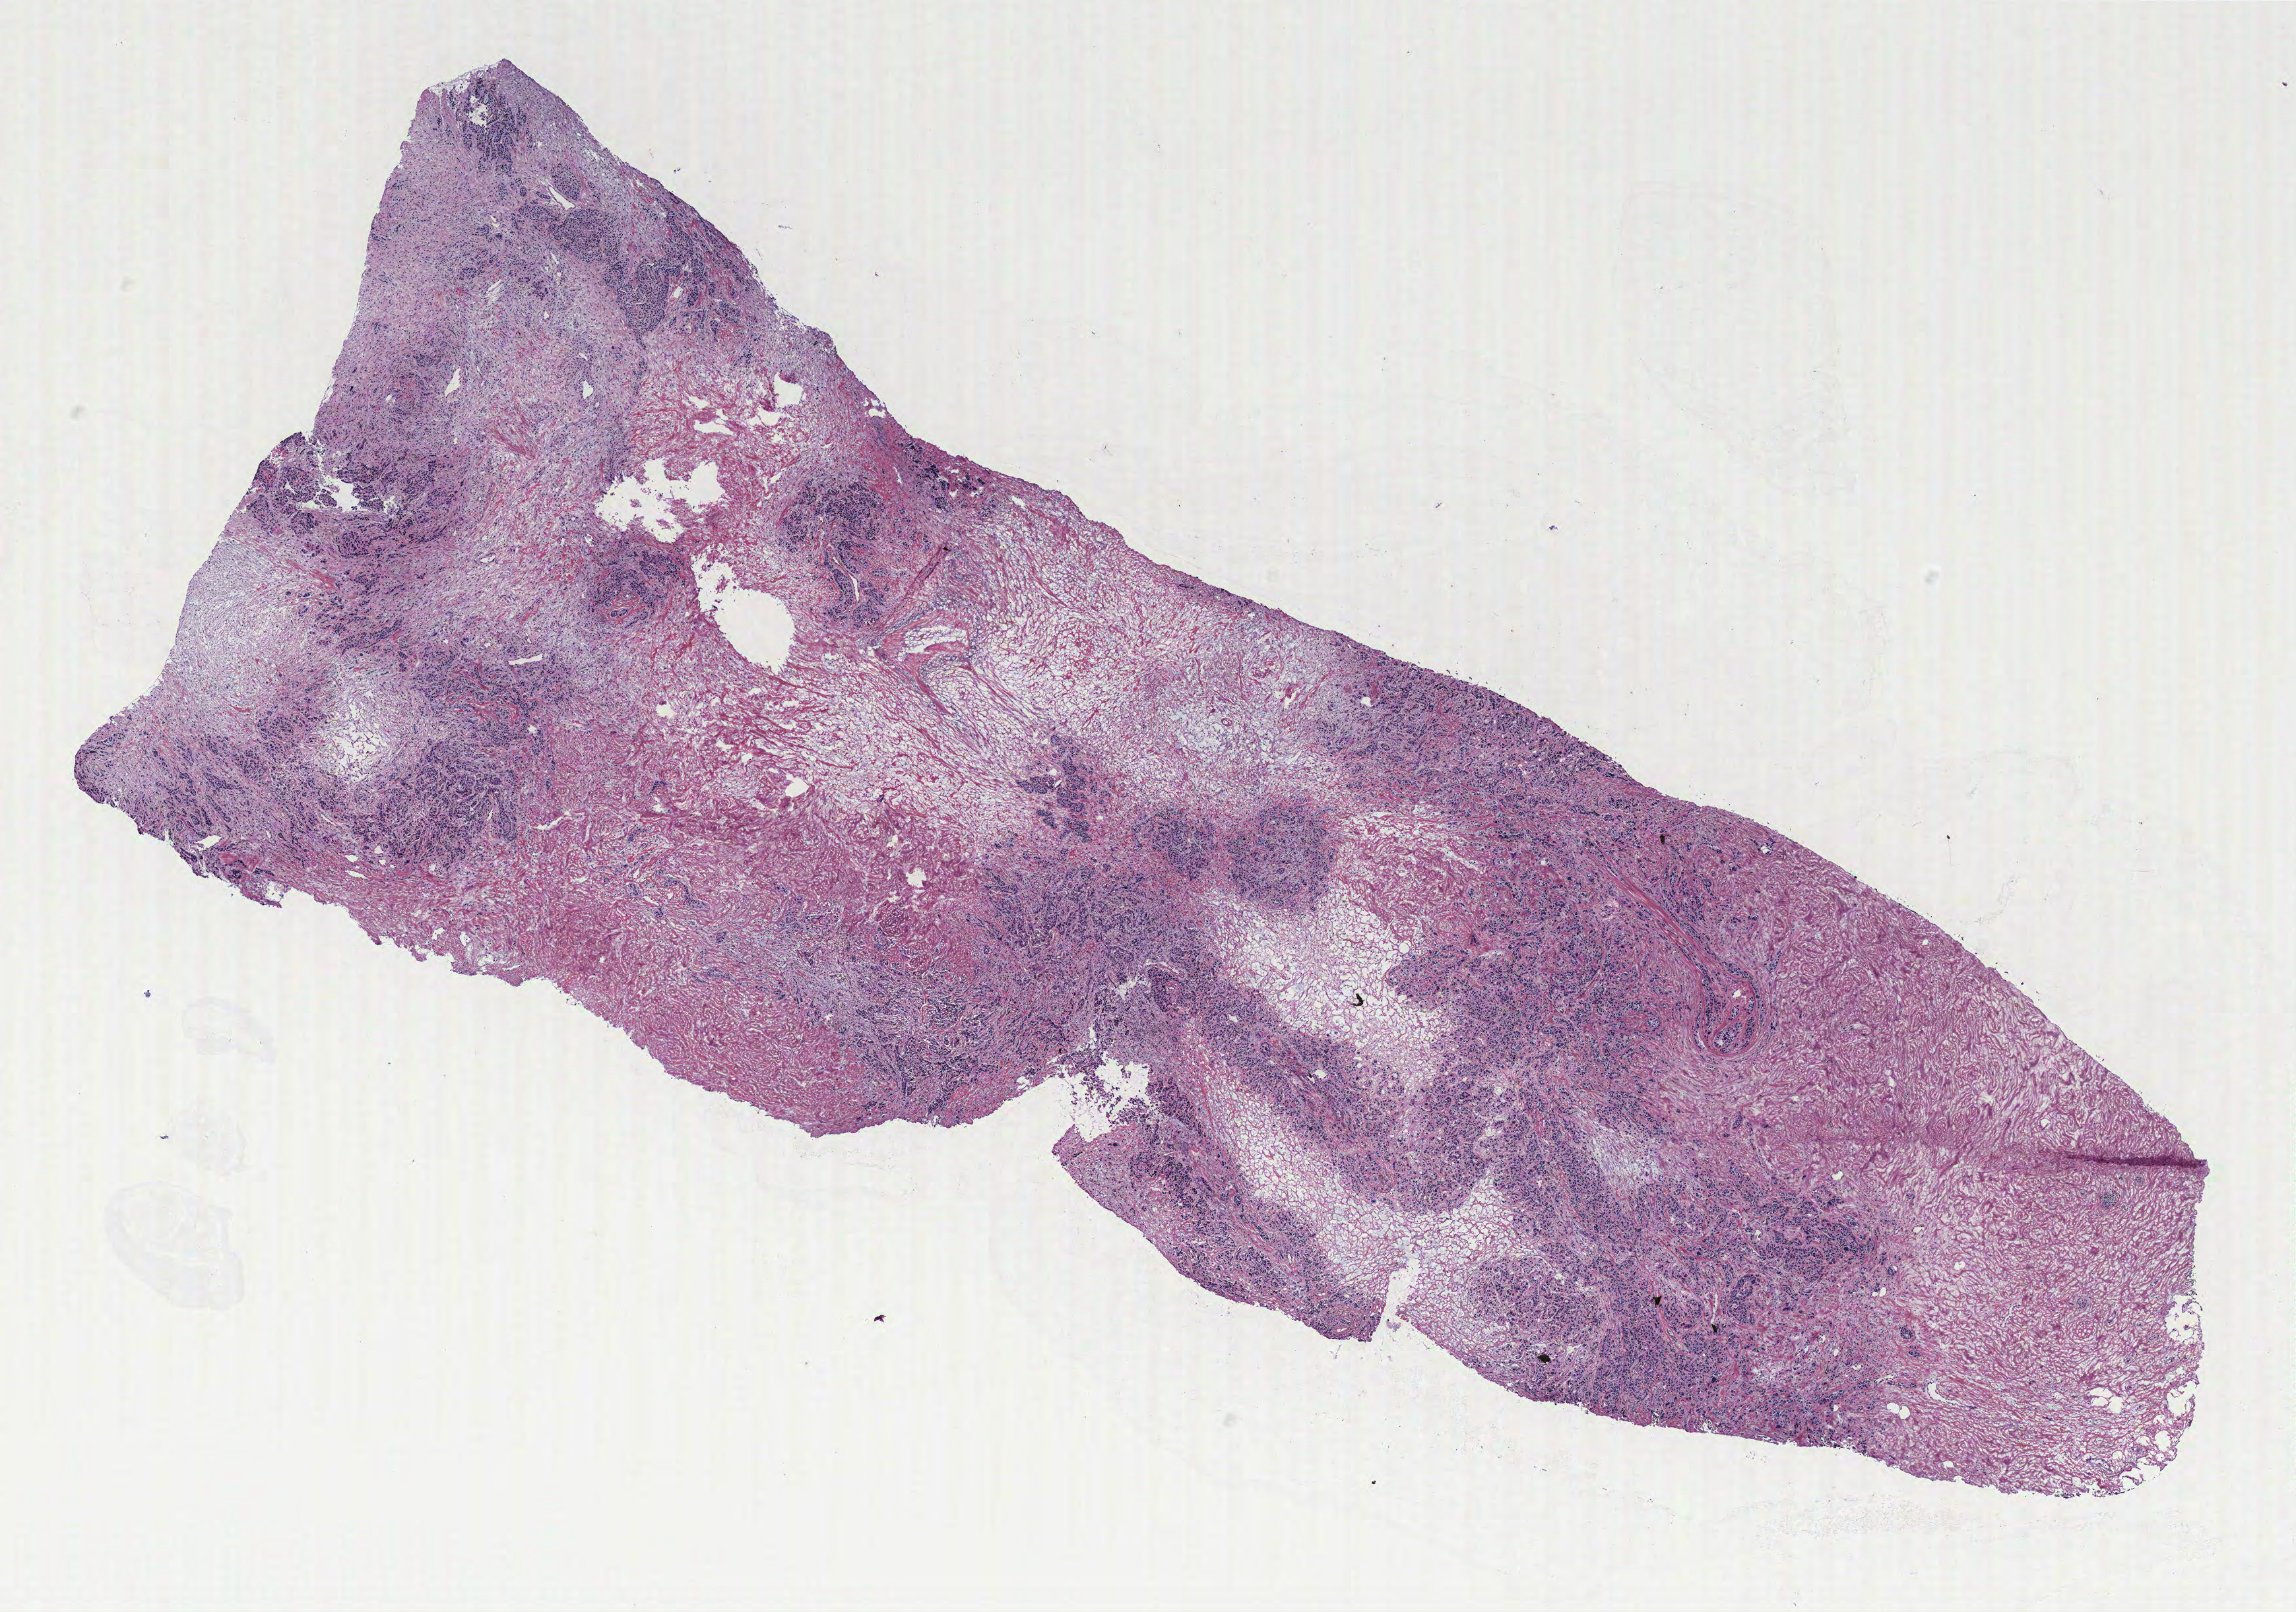
Whole-slide histology image, Hematoxylin and eosin (H&E) stained — shown as a low-resolution overview of the whole scanned area (about 13.9 x 9.8 mm). Breast, tissue type not recorded. Patient: female, aged 90 or older.
Patient diagnosis: Infiltrating duct carcinoma, NOS.